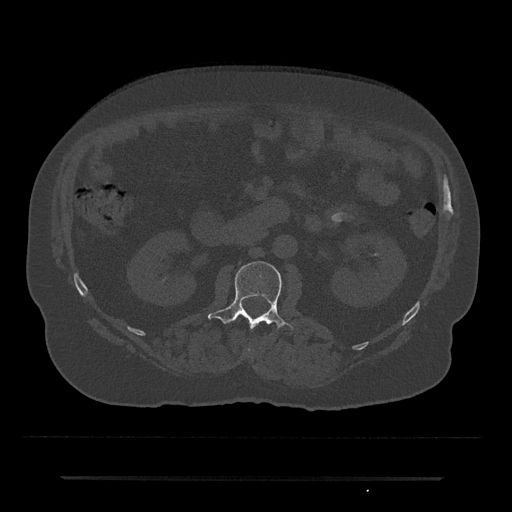
CT including the spine, one axial slice; slice 18 of 797 in the series (ordered by position); reconstruction kernel Br40s/3; 120 kVp; bone window (W 1800 / L 400 HU); 0.5 mm slice thickness; 512 × 512 image matrix. Male patient, age 69 years. Case-level facts recorded for this patient, not image findings: primary cancer: prostate.
Structures marked on this image (semi-automatic segmentation, software-assisted and operator-edited):
- L1 vertebra: box from (x=248, y=348) to (x=251, y=352) px
- L2 vertebra: (x=208, y=261)–(x=293, y=330)